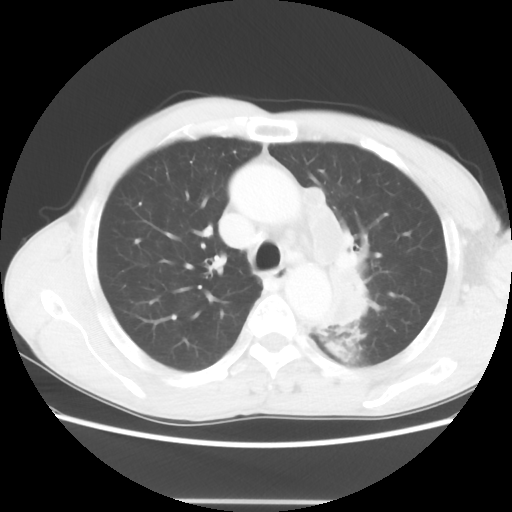
Chest CT, one axial slice. Position 45 of 62 along the scan axis. Reconstruction kernel STANDARD. Lung window (W 1500 / L -600 HU). 512 × 512 image matrix. Male patient, age 61 years. Case-level facts recorded for this patient, not image findings: clinical TNM (as recorded): T3 N1 M1.
Annotated regions visible in this slice (rectangle marked by the reading radiologist):
- lung tumour (recorded histology: adenocarcinoma): box from (x=301, y=190) to (x=369, y=334) px